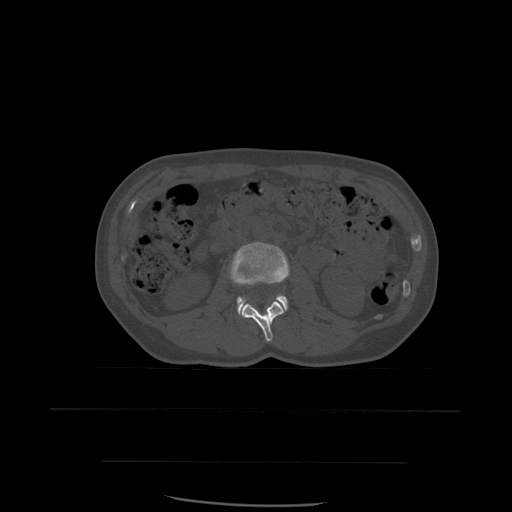
CT including the spine, one axial slice. Position 212 of 574 along the scan axis. Bone window (W 1800 / L 400 HU). 1.25 mm slice thickness. 512 × 512 image matrix. Patient age 48 years. Case-level facts recorded for this patient, not image findings: primary cancer: lung; vertebrae with lytic lesions (as recorded): T11.
Outlined on this slice (semi-automatic segmentation, software-assisted and operator-edited):
- L2 vertebra: bounding box [x1, y1, x2, y2] px = [239, 302, 285, 343]
- L3 vertebra: [230, 242, 290, 314]